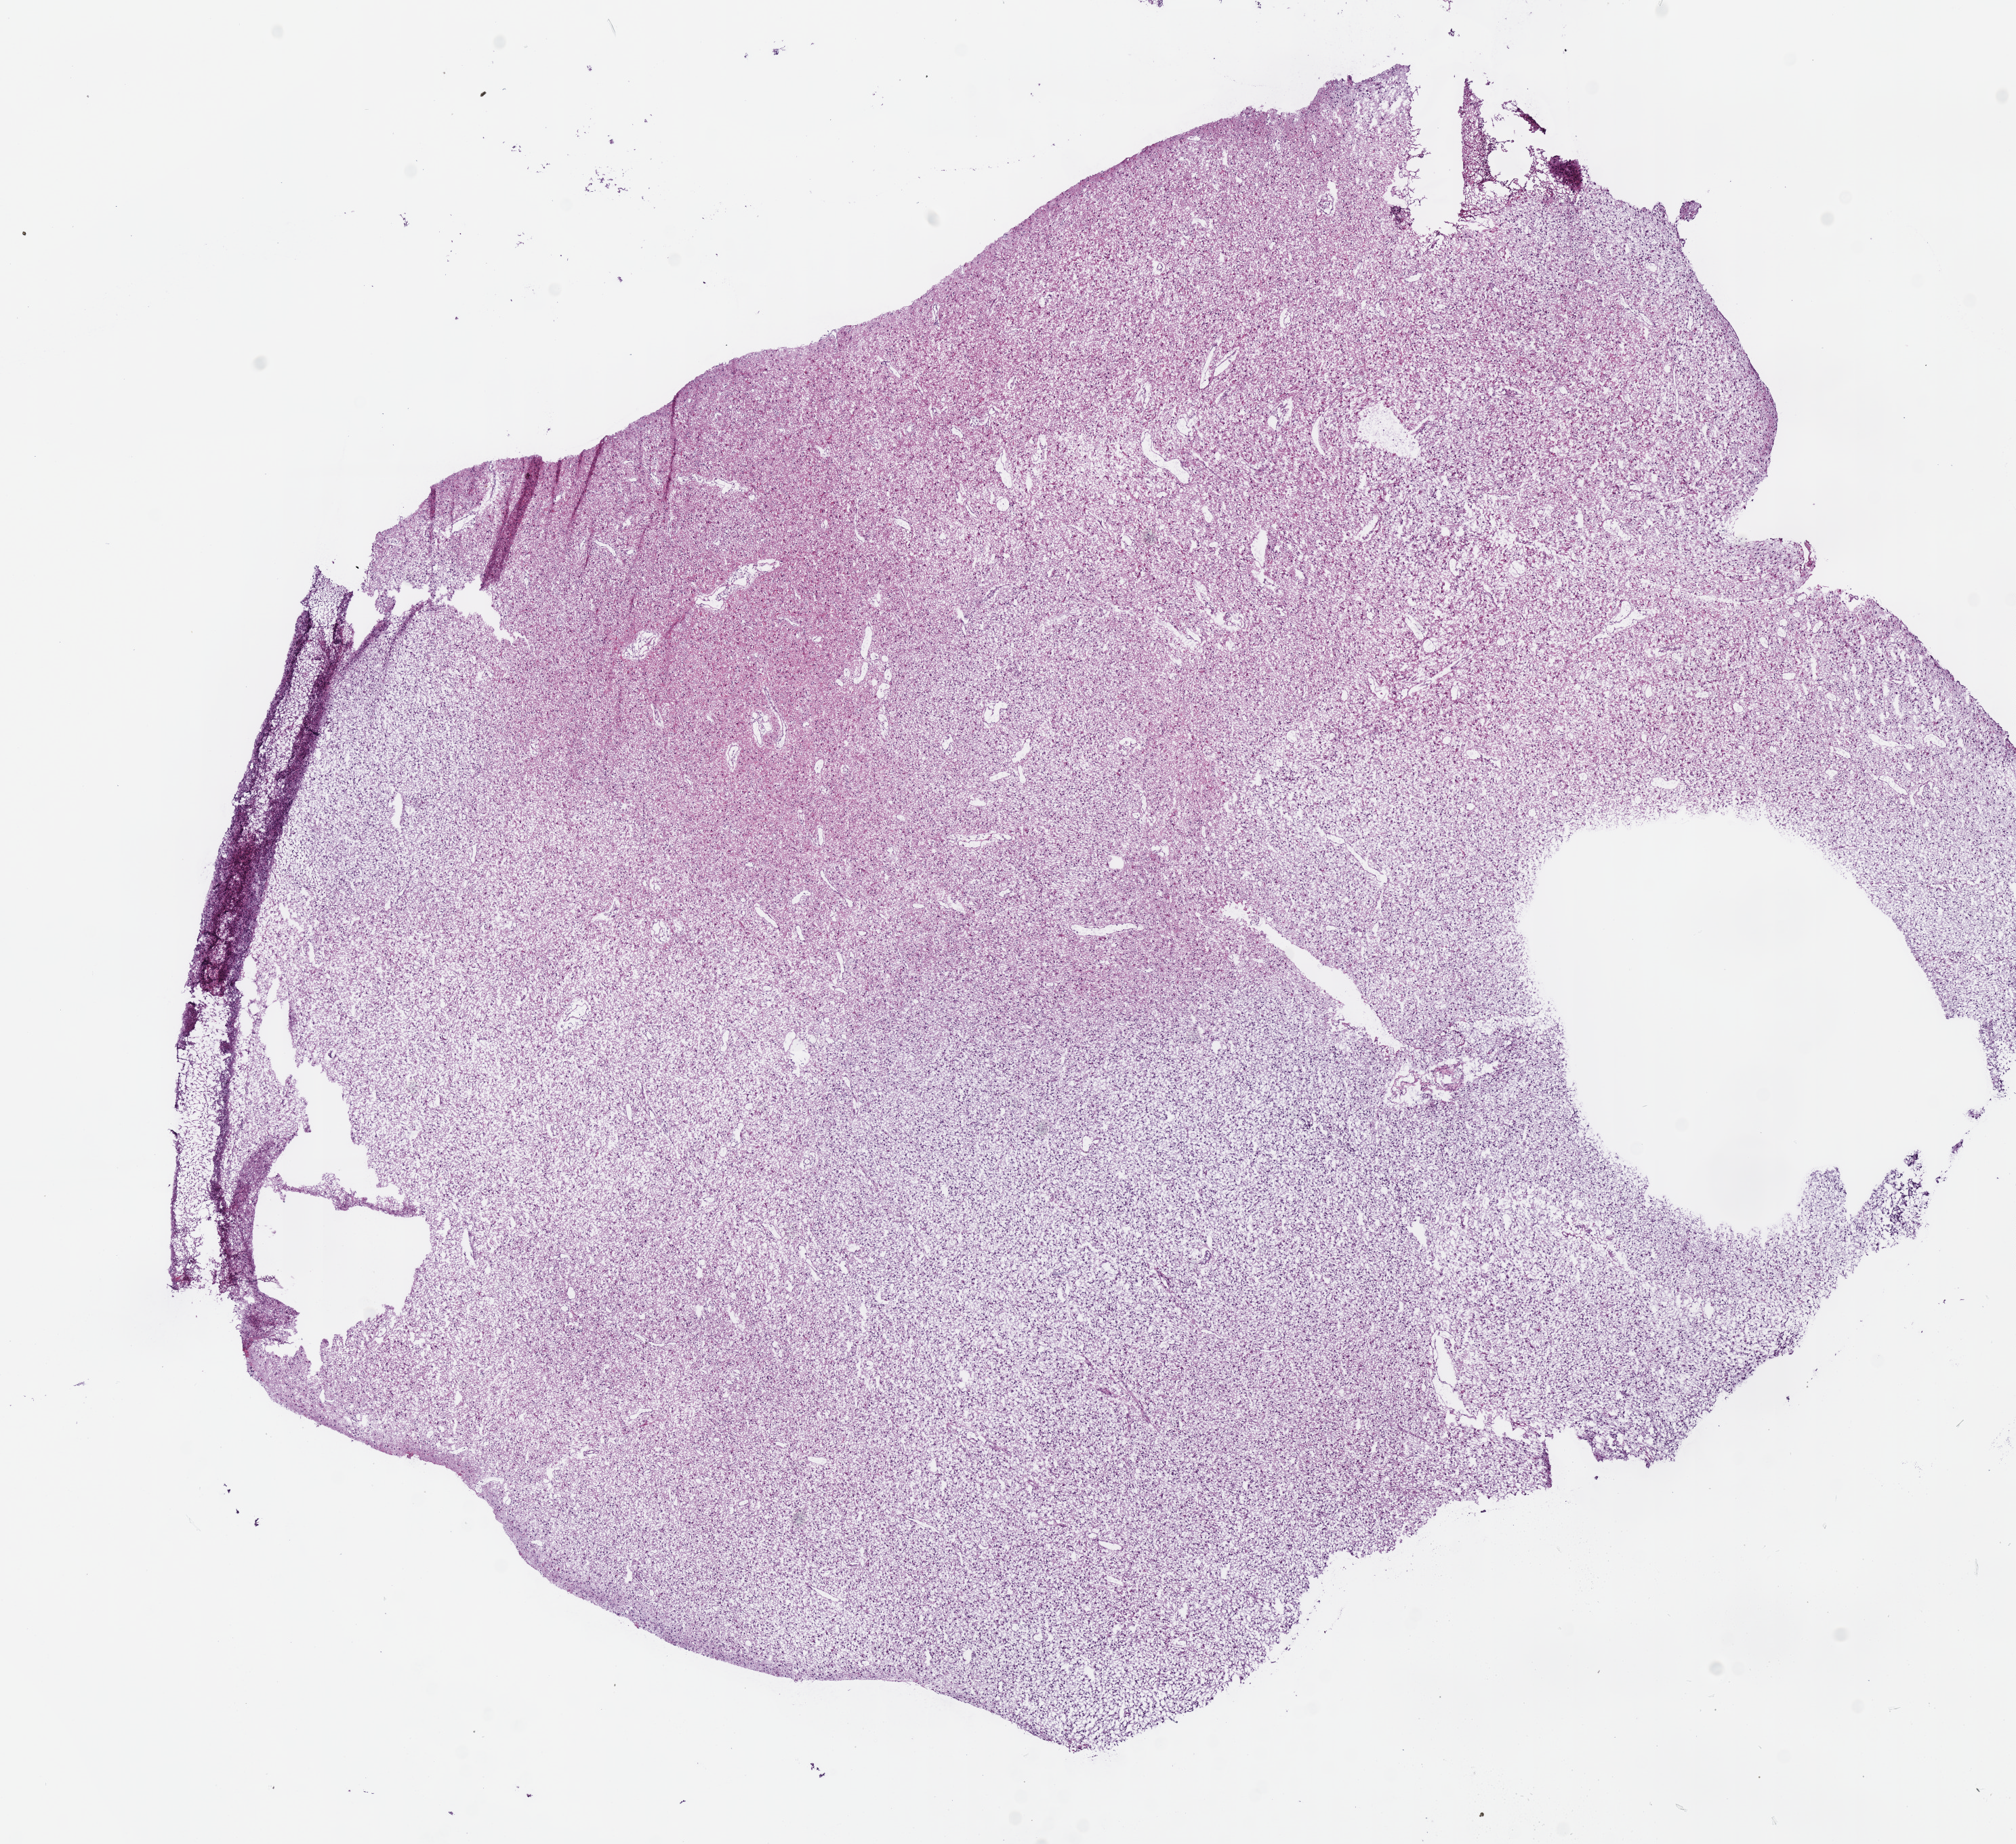
Digitized Hematoxylin and eosin (H&E) stained tissue section (whole slide), whole scanned area (about 11.7 x 10.7 mm, acquisition: 40x scan) shown as a low-resolution overview, frozen section from the bottom of the tissue portion, primary tumour sample from the brain. Male, age 43 years at initial diagnosis. Histologic grade: G2 (moderately differentiated). Pathologist review of this section (percent, as recorded): tumour cells 100%, tumour nuclei 75%, normal cells 0%, stromal cells 0%, necrosis 0%.
Diagnosis: Mixed glioma (cerebrum). Laterality: left.